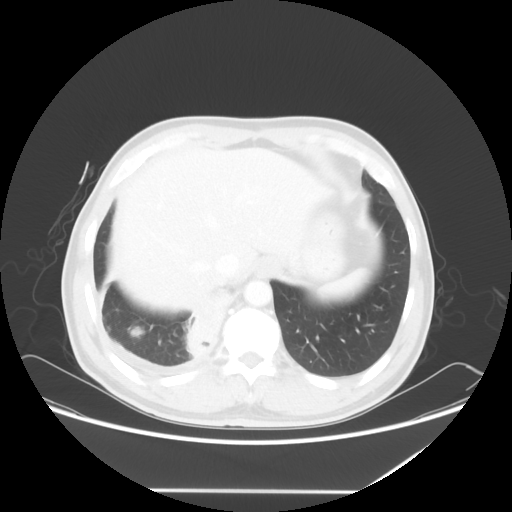
Chest CT, one axial slice; slice 12 of 60 in the series (ordered by position); reconstruction kernel STANDARD; lung window (W 1500 / L -600 HU); 512 × 512 image matrix, field of view 419 × 419 mm. Male patient, age 48 years. Case-level facts recorded for this patient, not image findings: clinical TNM (as recorded): T3 N3 M1a.
Outlined on this slice (bounding box drawn by a radiologist):
- lung tumour (recorded histology: squamous cell carcinoma): bounding box [x1, y1, x2, y2] px = [183, 283, 236, 358]